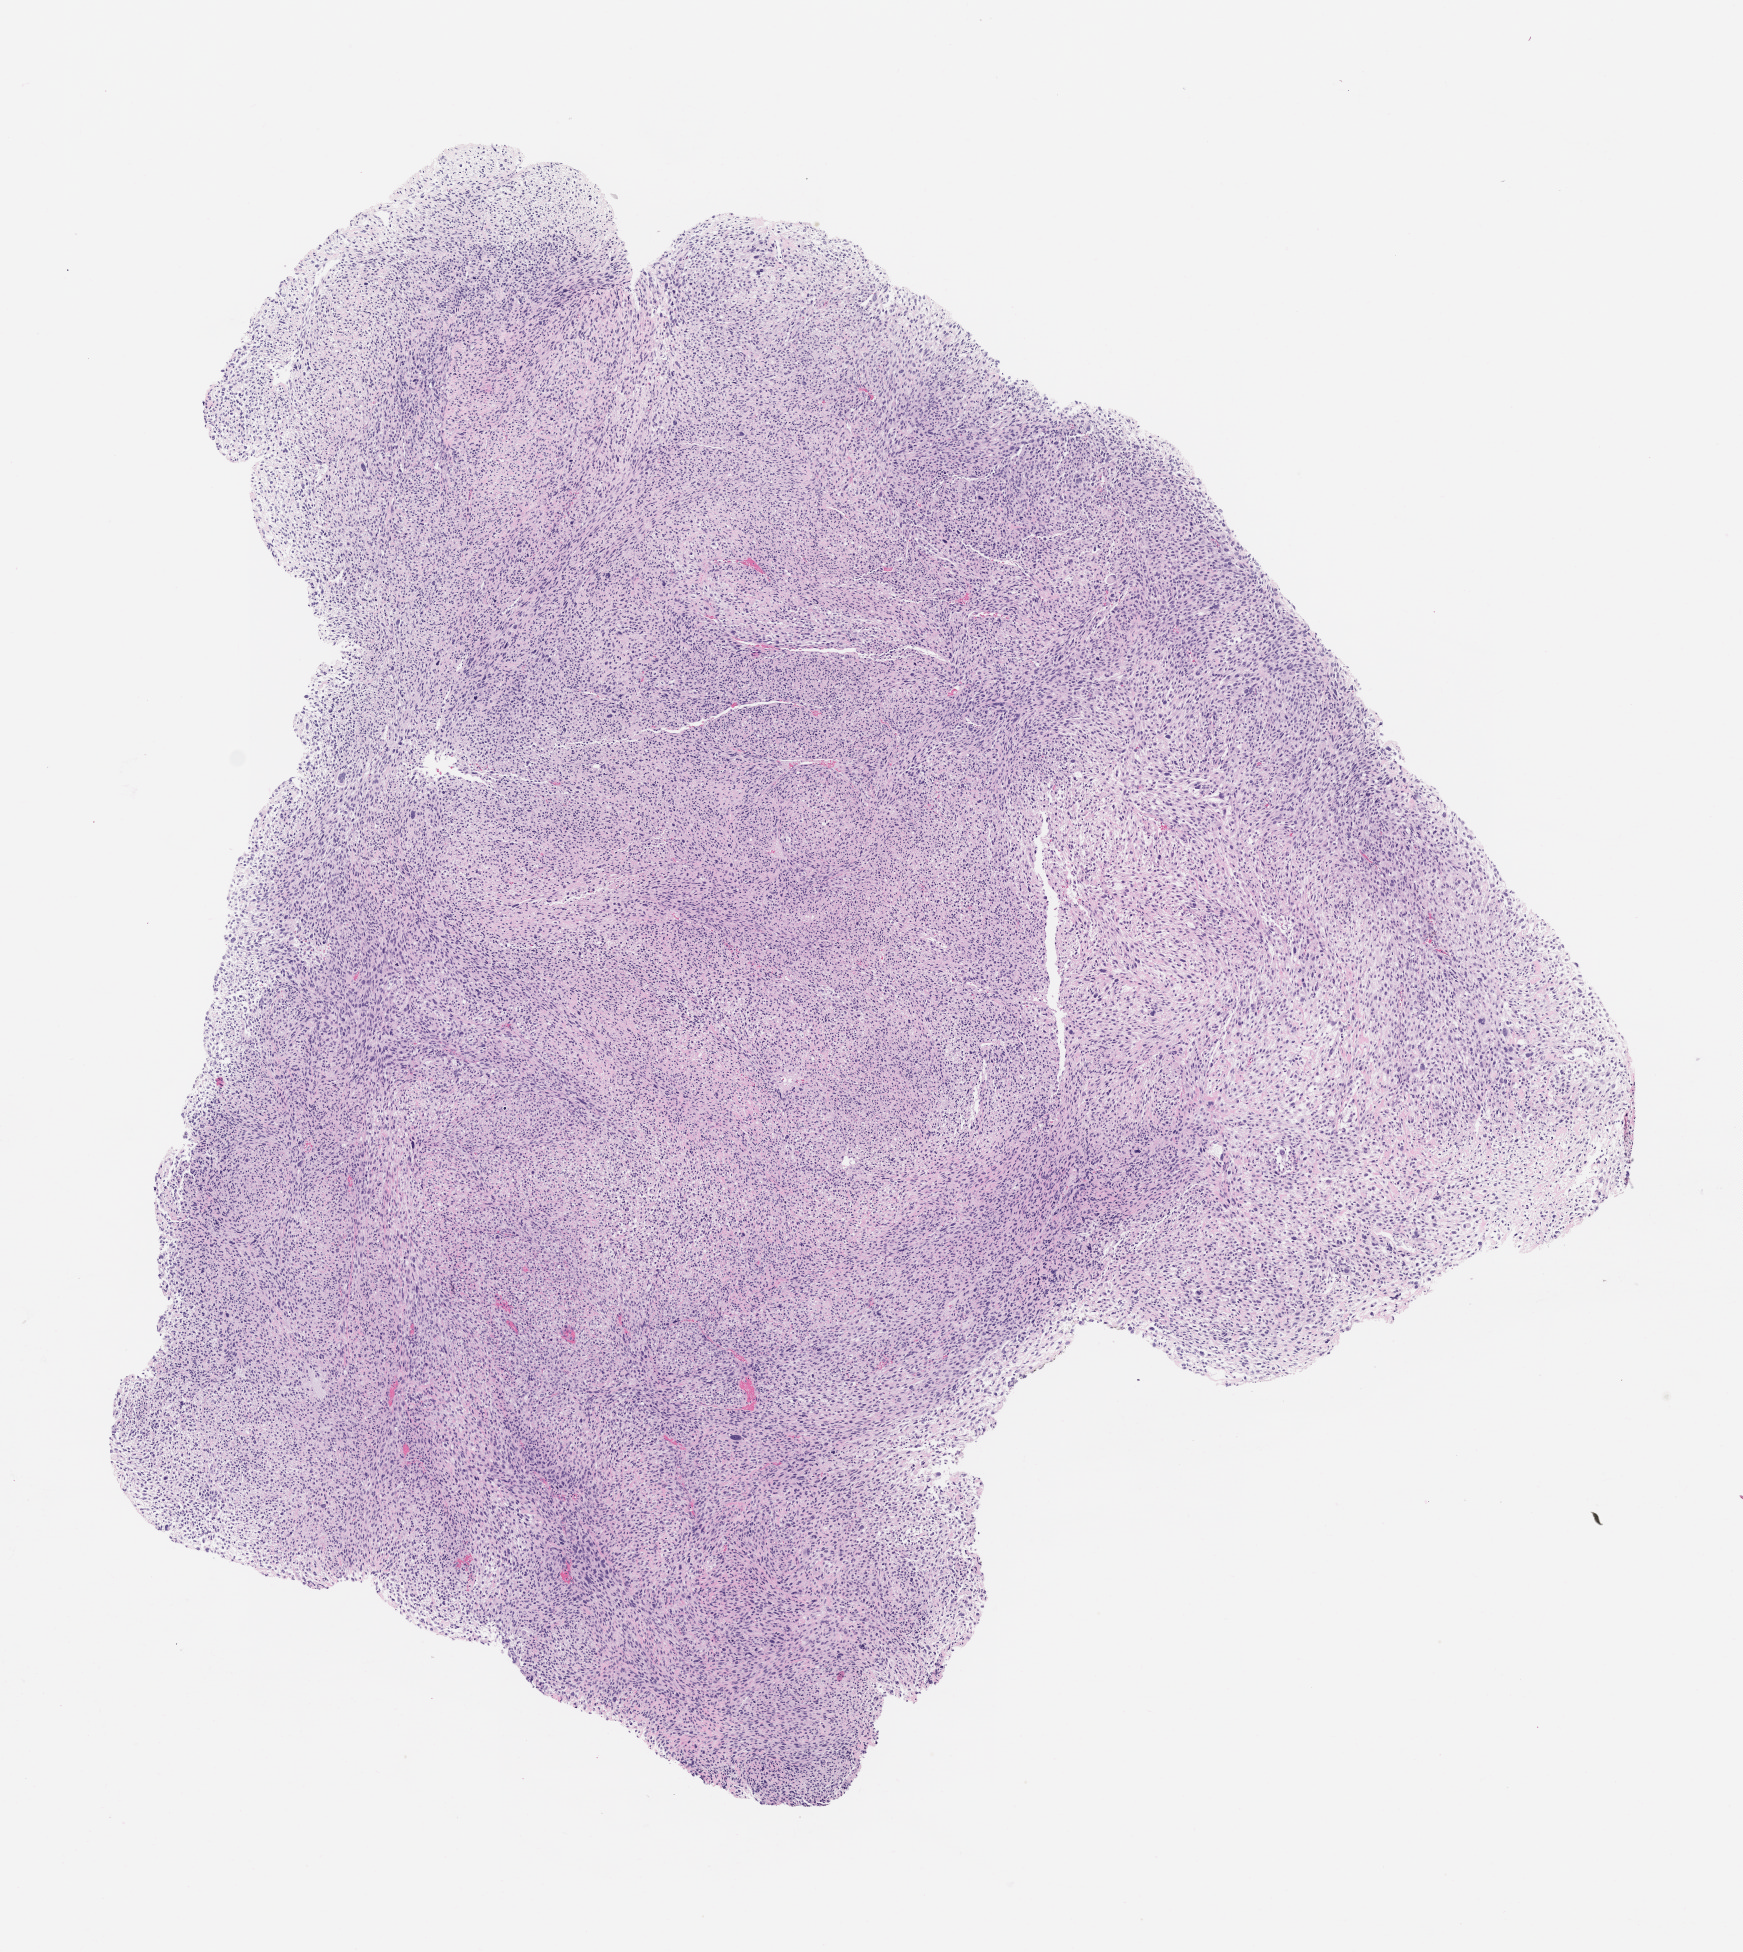
Whole-slide image, hematoxylin and eosin (H&E) stain of the patient's (originator) tumor tissue, shown as a low-resolution overview of the whole scanned area (about 7.0 x 7.9 mm); formalin-fixed paraffin-embedded section; tumor site category: musculoskeletal. Patient: male, 67 years old.
* diagnosis: Non-Rhabdo. soft tissue sarcoma